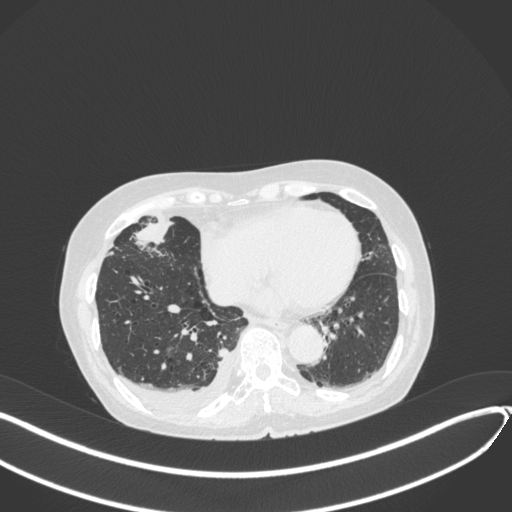
Chest CT, one axial slice. Slice 126 of 418 in the series (ordered by position). 120 kVp. Lung window (W 1500 / L -600 HU). 512 × 512 image matrix, field of view 400 × 400 mm. Female patient, age 75 years. Case-level facts recorded for this patient, not image findings: clinical TNM (as recorded): T2a N3 M0.
Structures marked on this image (bounding box drawn by a radiologist):
- lung tumour (recorded histology: adenocarcinoma): bounding box [x1, y1, x2, y2] px = [133, 213, 176, 251]